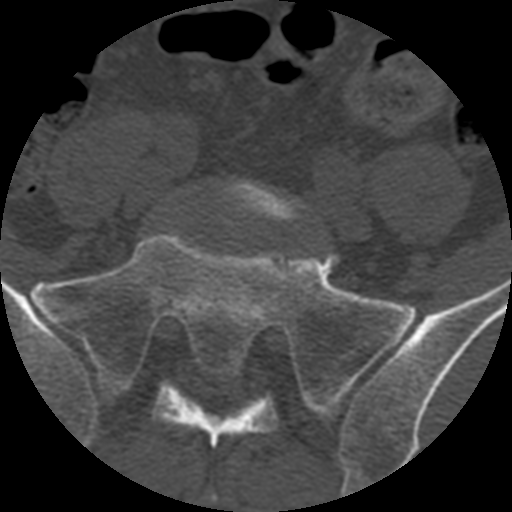
CT including the spine, one axial slice; slice 234 of 399 in the series (ordered by position); reconstruction kernel STANDARD; 120 kVp; bone window (W 1800 / L 400 HU); 1.25 mm slice thickness; 512 × 512 image matrix, field of view 160 × 160 mm. Patient age 71 years. Case-level facts recorded for this patient, not image findings: primary cancer: prostate.
Annotated regions visible in this slice (semi-automatic segmentation, software-assisted and operator-edited):
- L5 vertebra: box from (x=221, y=181) to (x=308, y=224) px